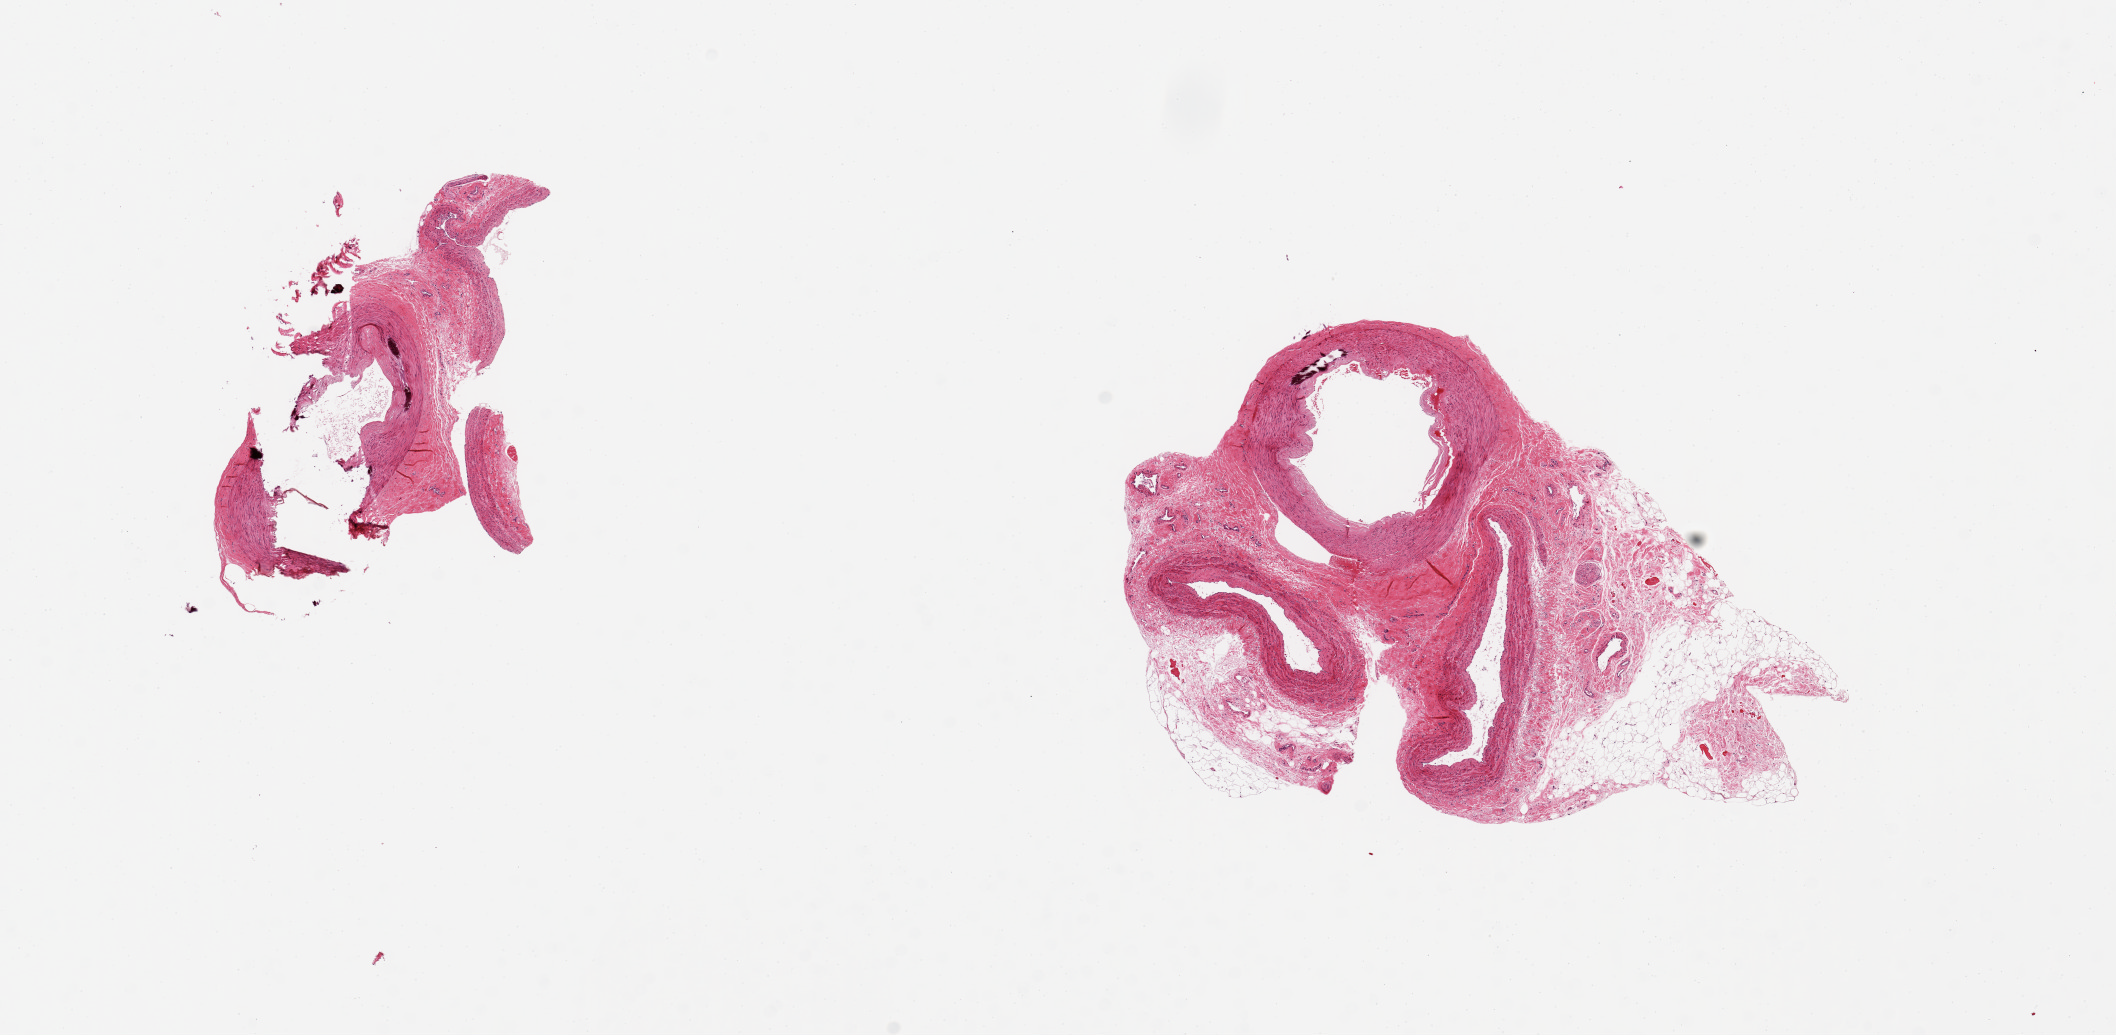
H&E whole-slide image, low-resolution overview of the scanned area, about 16.7 x 8.2 mm, PAXgene-fixed, paraffin-embedded tissue, sampled site (target tissue): tibial artery, donor tissue sample. Donor: female.
Pathologist's review note for this sample: 2 pieces, 4x3 & 6x4mm; 1 has artery + 2 veins and 30% adherent stroma; other artery is fragmented; both contain medial calcification.